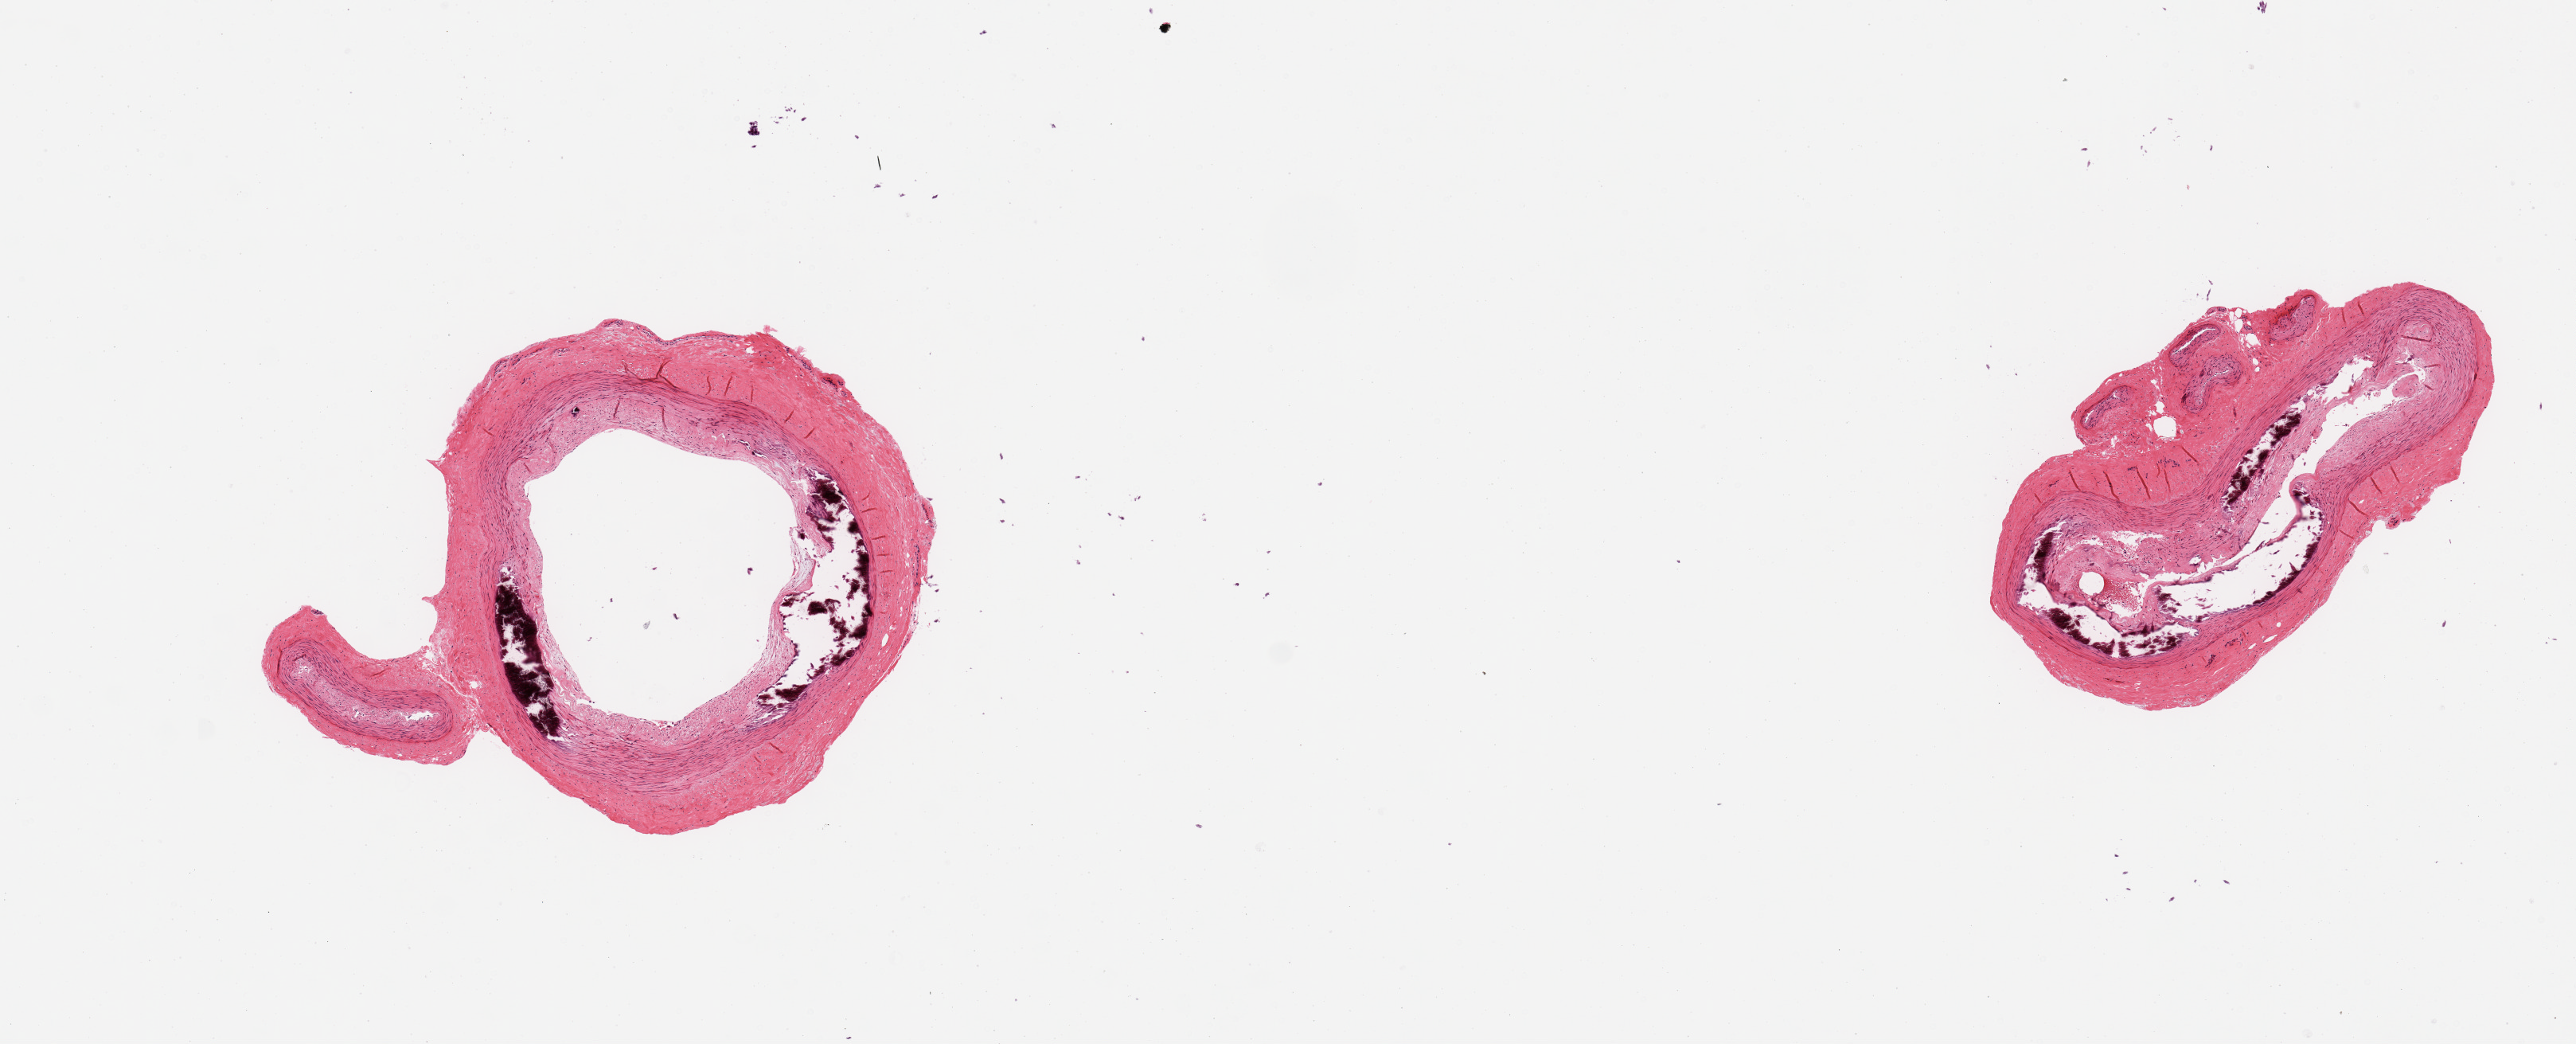
Digitized haematoxylin and eosin-stained section, brightfield — a low-resolution overview of the entire scanned area, about 12.8 x 5.2 mm. PAXgene-fixed paraffin-embedded (PFPE) section. Target tissue: tibial artery. Donor tissue sample. Male donor.
* reviewer comment on this tissue sample: 2 pieces, clean specimens, calcifying atheromatous debris, ~40% occlusive